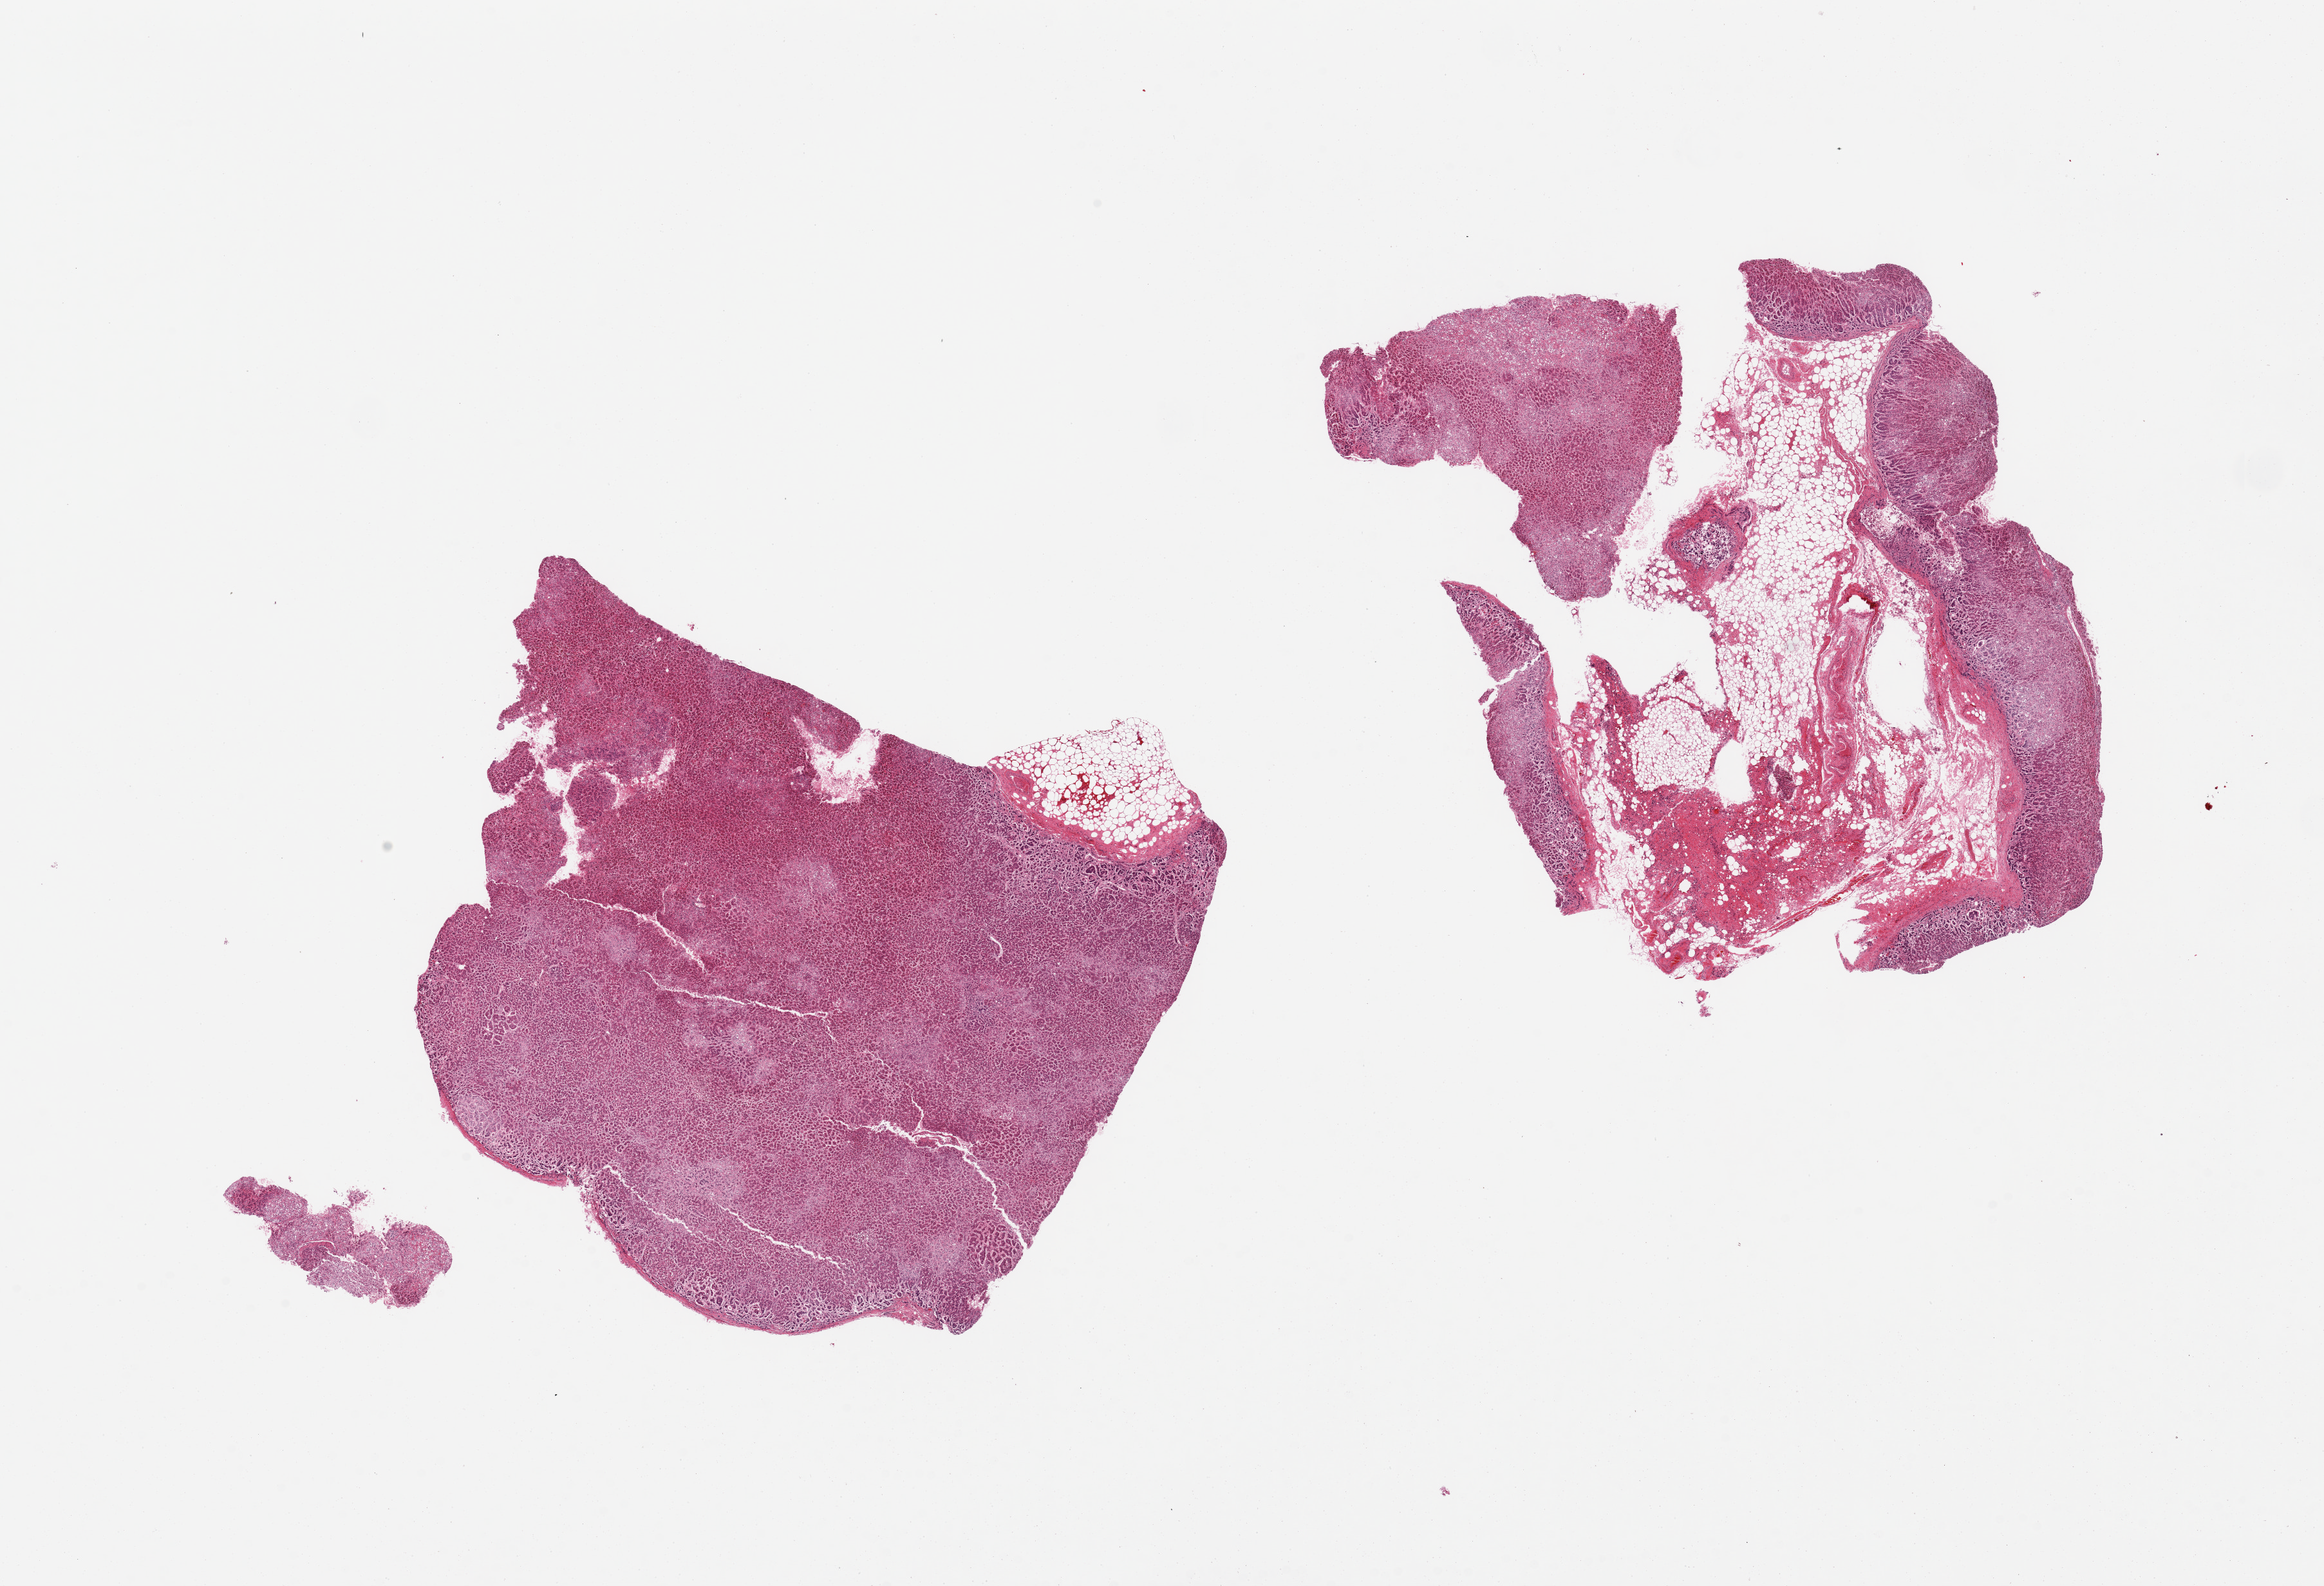
Digitized H&E-stained section, low-resolution overview of the scanned area, about 28.5 x 19.5 mm (from a 20x scan). PAXgene-fixed paraffin-embedded (PFPE) section. Sampled site (target tissue): adrenal gland. Tissue donor sample. Donor sex: female.
- review note (as recorded): 2 pieces, all cortex, badly autolyzed; One aliquot is ~50% adherent fat